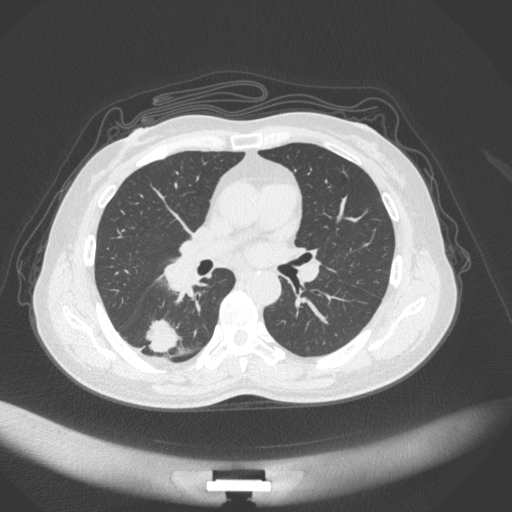
Chest CT, one axial slice. Slice 166 of 352 in the series (ordered by position). Reconstruction kernel B31f. 120 kVp. Lung window (W 1500 / L -600 HU). 1 mm slice thickness. 512 × 512 image matrix, field of view 400 × 400 mm. Patient: female, 55 years. From the clinical record (not read from this slice): clinical TNM (as recorded): T1c N1 M0.
Outlined on this slice (bounding box drawn by a radiologist):
- lung tumour (recorded histology: adenocarcinoma): bounding box [x1, y1, x2, y2] px = [144, 318, 180, 355]